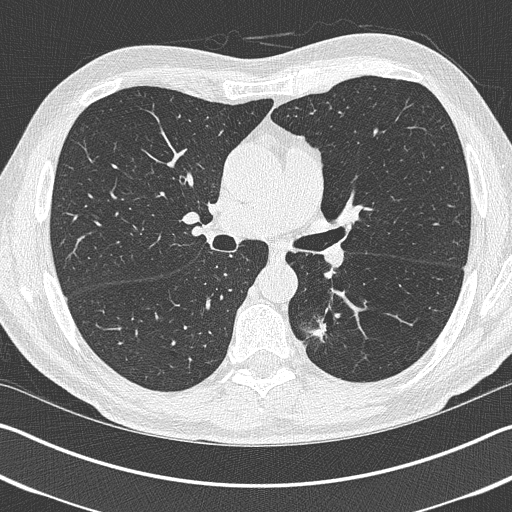
Low-dose screening chest CT, one axial slice. Position 242 of 402 along the scan axis. Reconstruction kernel B50f. Lung window (W 1500 / L -600 HU). 1 mm slice thickness. 512 × 512 image matrix, field of view 340 × 340 mm.
Structures marked on this image (outlined manually by an expert reader):
- lesion 1 (tumor, lower lobe of left lung): box from (x=310, y=320) to (x=327, y=341) px